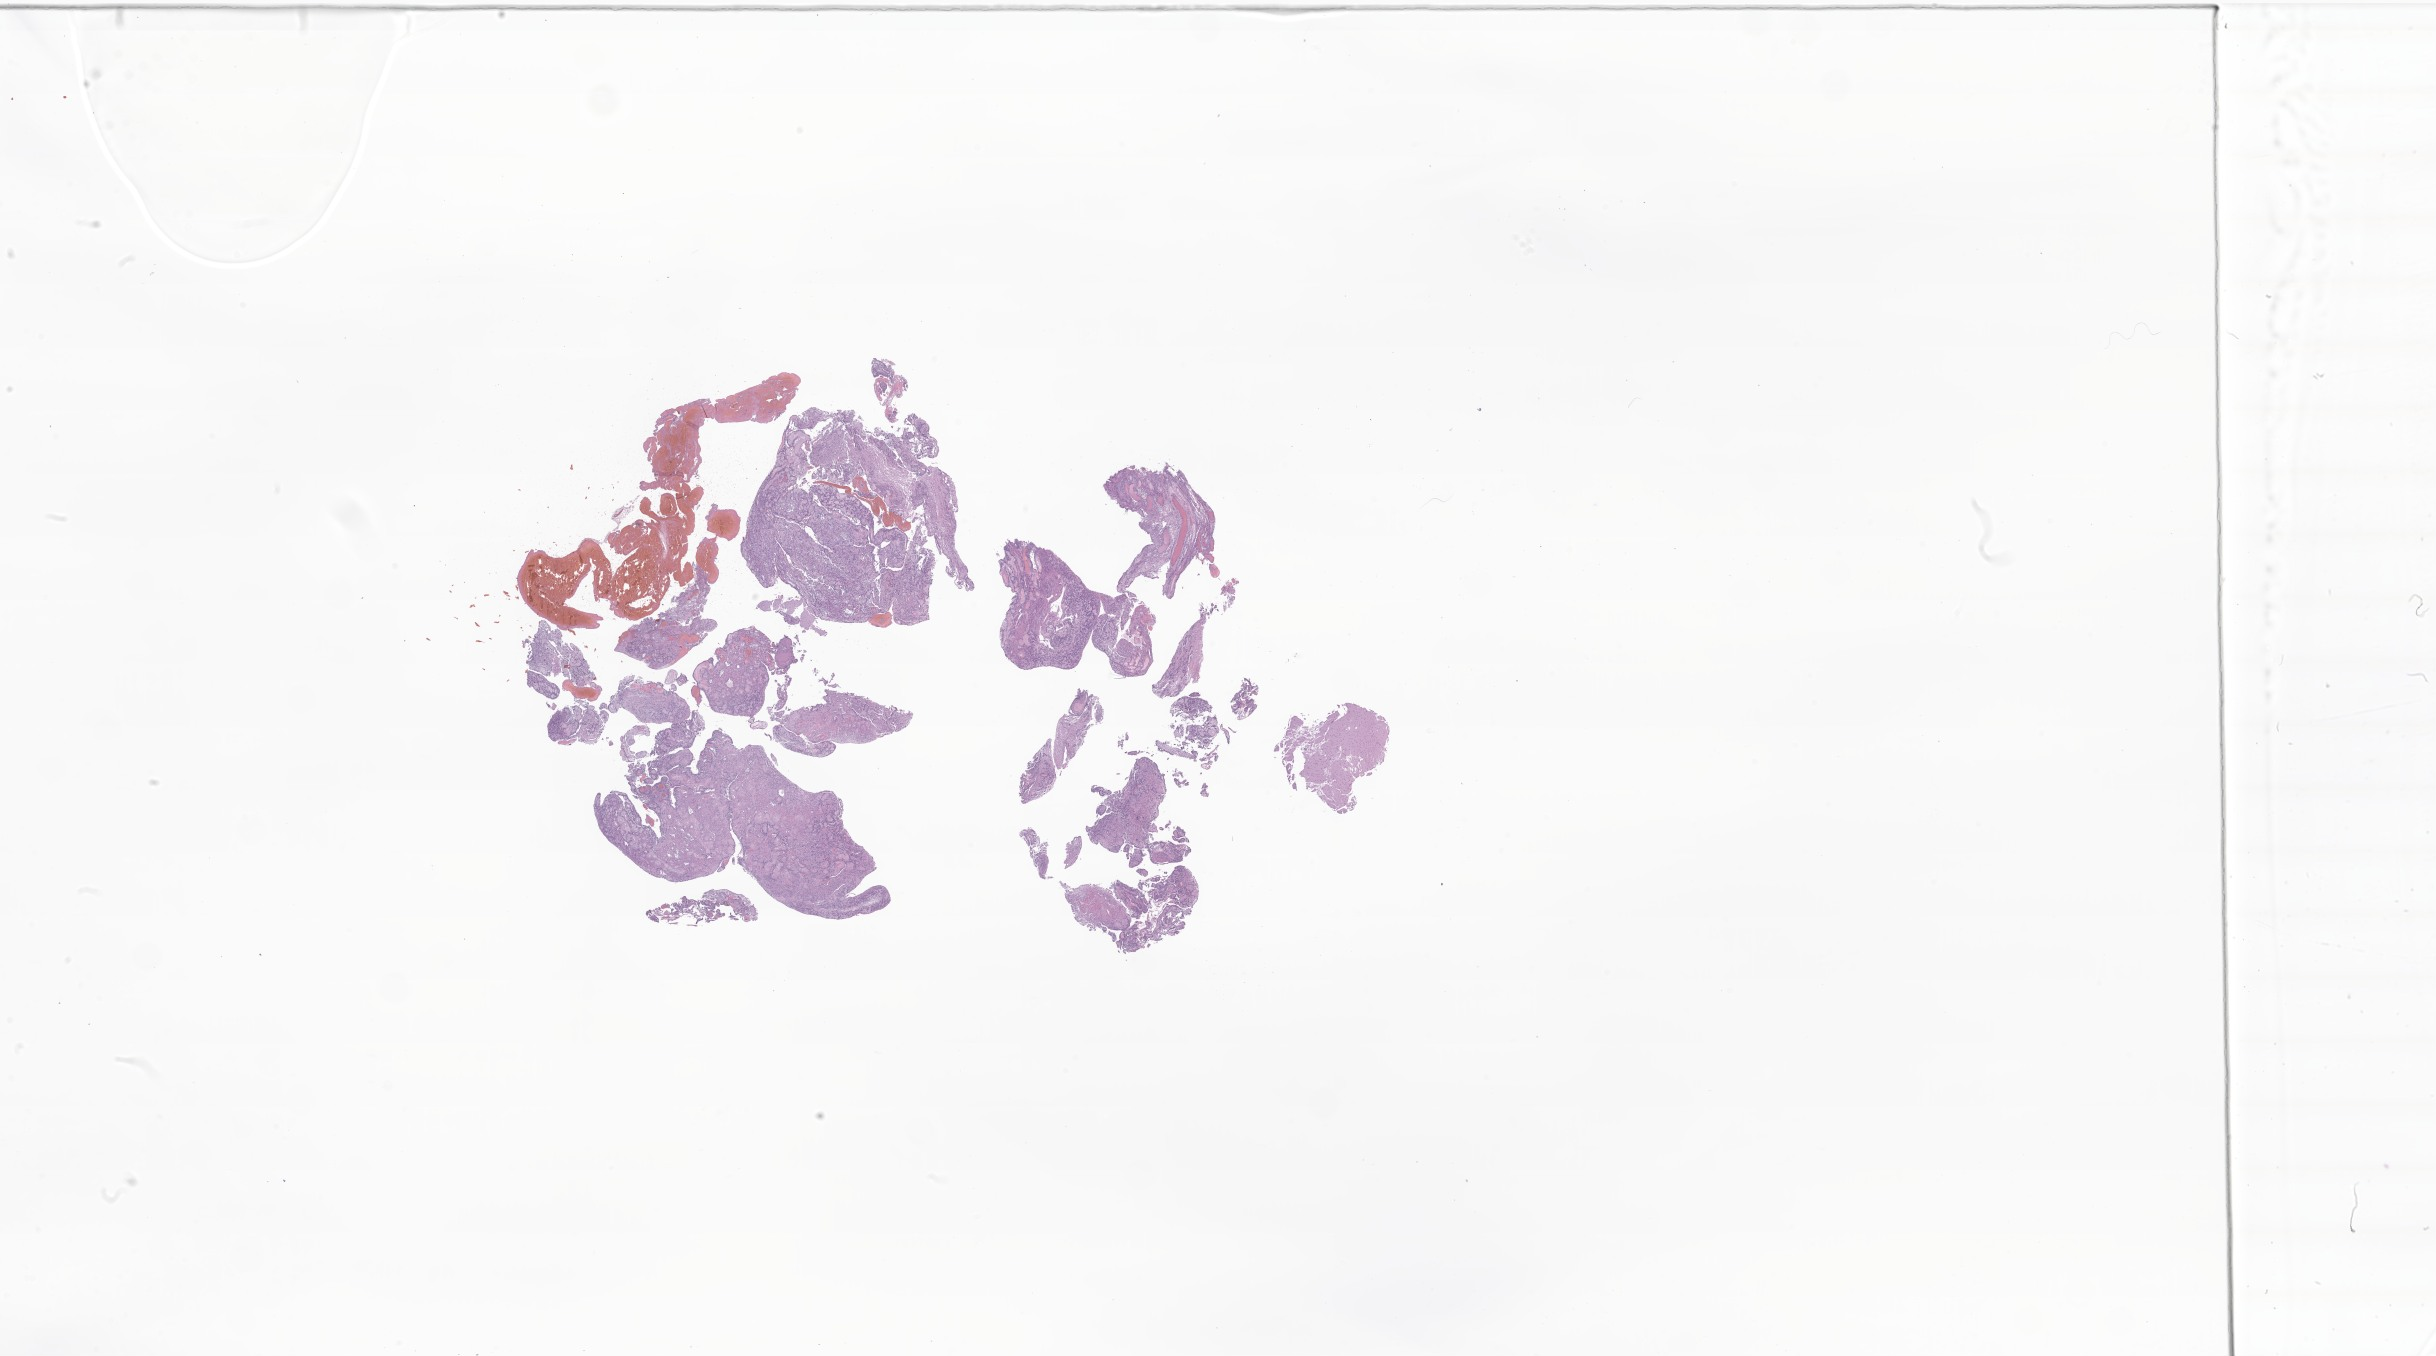
Whole-slide image, H&E stain of tumor tissue from the frontal lobe, low-resolution overview of the scanned area, about 41.1 x 22.9 mm, FFPE section. Patient: female, age 198 months.
Diagnosis: Papillary glioneuronal tumor.